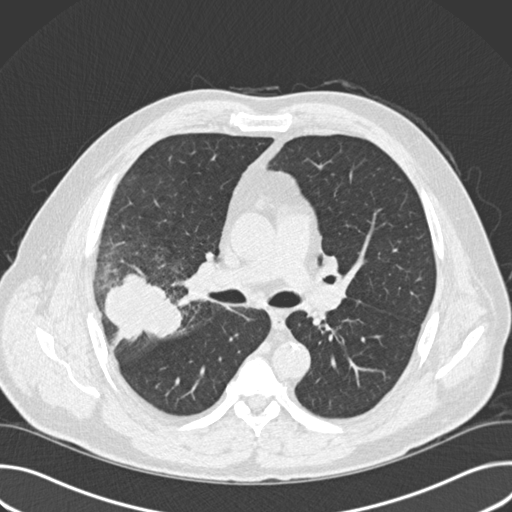
Low-dose screening chest CT, one axial slice; position 98 of 157 along the scan axis; reconstruction kernel B30f; 120 kVp; lung window (W 1500 / L -600 HU); 2 mm slice thickness; 512 × 512 image matrix.
Annotated regions visible in this slice (expert manual segmentation):
- lesion 1 (tumor, upper lobe of right lung): bounding box [x1, y1, x2, y2] px = [104, 273, 183, 342]